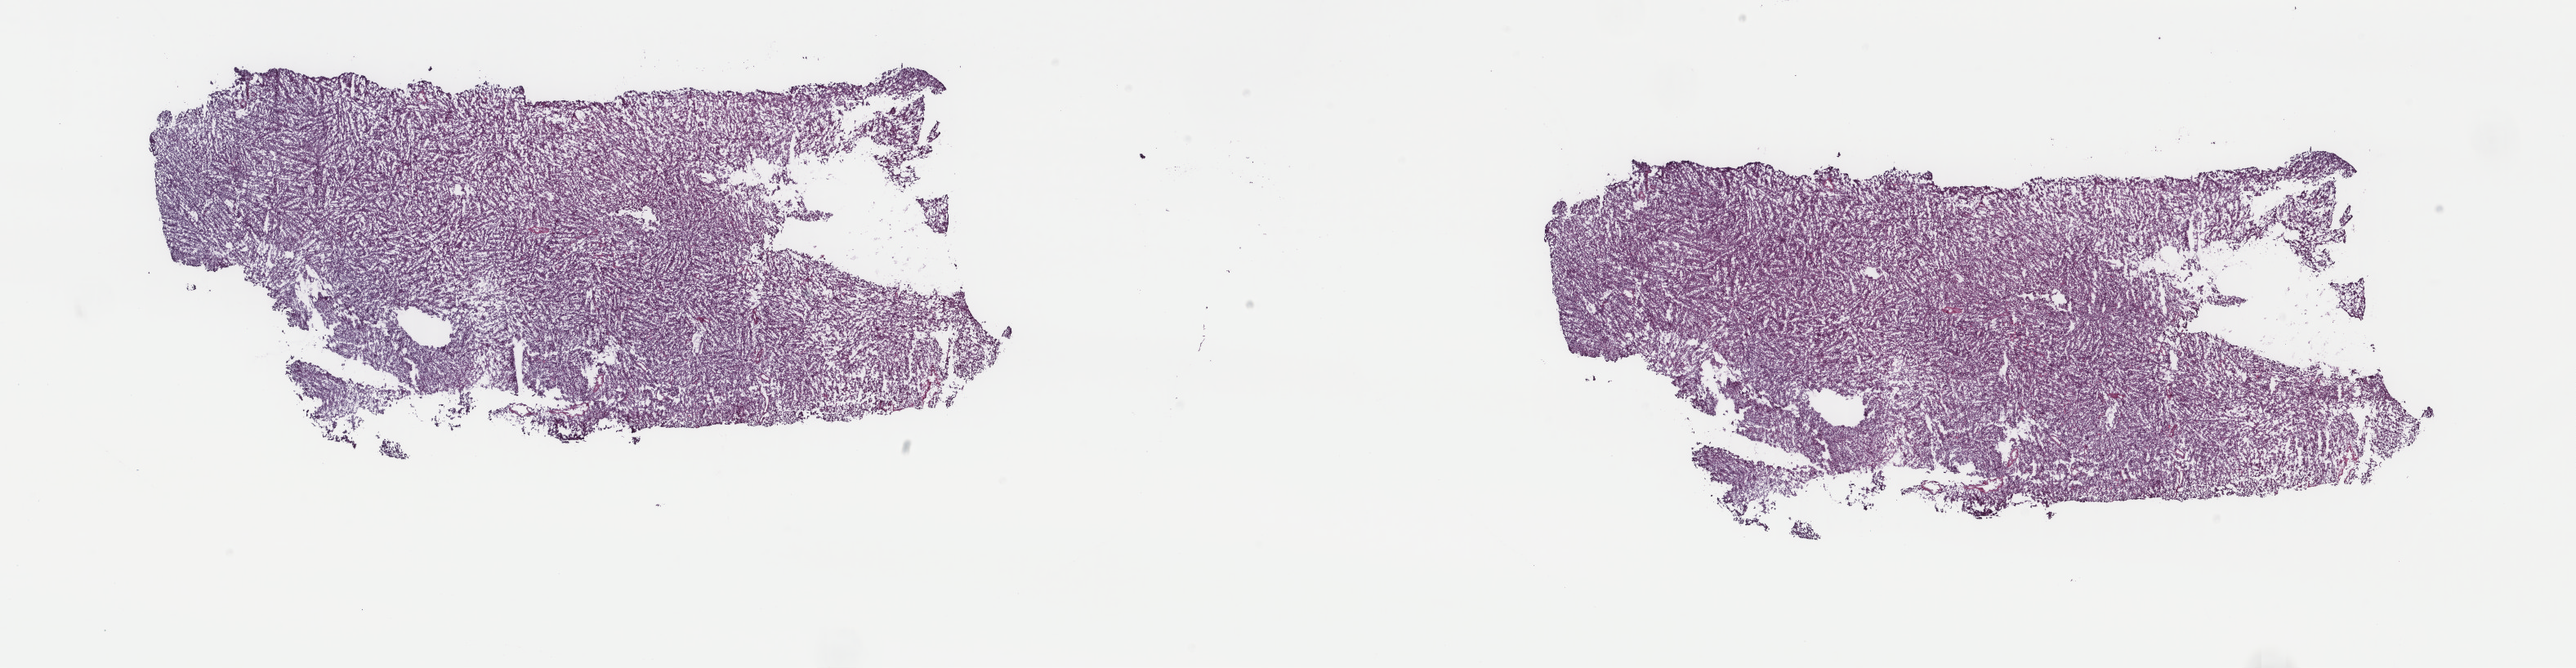
Hematoxylin and eosin (H&E) stained whole-slide image — whole scanned area (about 25.0 x 6.5 mm, acquisition: 40x scan) shown as a low-resolution overview; frozen section from the top of the tissue portion; sample: primary tumour, uterus. Female, age 48 years at initial diagnosis. Slide review estimates, as recorded: tumour cells 95%, tumour nuclei 95%, normal cells 0%, stromal cells 0%, necrosis 5%. Inflammatory infiltration, as recorded: lymphocyte infiltration 5%, monocyte infiltration 0%, neutrophil infiltration 0%.
* histologic diagnosis: Leiomyosarcoma, NOS